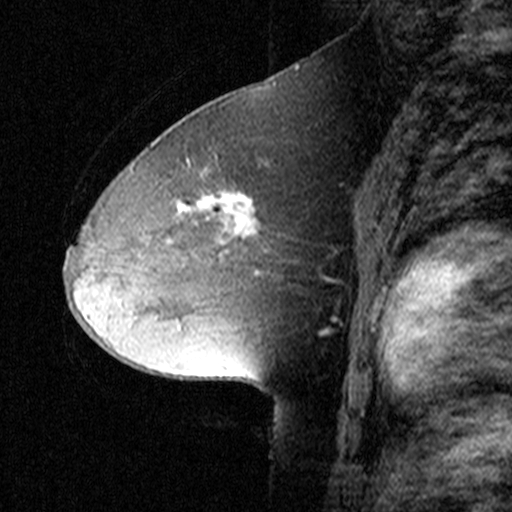
Breast MRI (dynamic contrast-enhanced), one sagittal slice; slice 21 of 44 in the series (ordered by position); dynamic contrast-enhanced study with each time point stored as its own series, time point 2 of 3 at this slice position (early post-contrast, ordered by acquisition time); 1.5 T; TE 4.5 ms, TR 11 ms; 512 × 512 image matrix, field of view 200 × 200 mm. Patient: female, 50 years. From the clinical record (not read from this slice): setting: breast cancer imaged before/during neoadjuvant chemotherapy; receptor status: HR-positive, HER2-negative.
Outlined on this slice (semi-automatic segmentation, software-assisted and operator-edited):
- analysis volume of interest (the breast-tissue region the enhancement analysis was run in; not a lesion): bounding box <154,164,313,287> (left, top, right, bottom; pixels)
- tumour enhancement mask (voxels above the 90 % enhancement threshold inside the analysis volume of interest): <205,194,254,236>